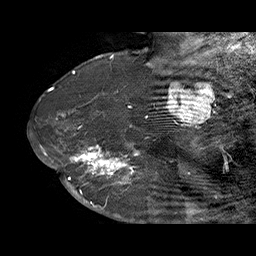
Breast MRI (dynamic contrast-enhanced), one sagittal slice. Position 47 of 70 along the scan axis. Dynamic contrast-enhanced series, time point 2 of 6 at this slice position (early post-contrast). 1.5 T. TE 4.5 ms, TR 32.4 ms. 3 mm slice thickness. 256 × 256 image matrix, field of view 180 × 180 mm. Female patient. From the clinical record (not read from this slice): setting: breast cancer imaged before/during neoadjuvant chemotherapy; receptor status: HR-positive, HER2-negative.
Structures marked on this image (semi-automatically segmented with operator editing):
- analysis volume of interest (the breast-tissue region the enhancement analysis was run in; not a lesion): bounding box [x1, y1, x2, y2] px = [71, 128, 159, 202]
- tumour enhancement mask (voxels above the 100 % enhancement threshold inside the analysis volume of interest): [71, 128, 155, 202]